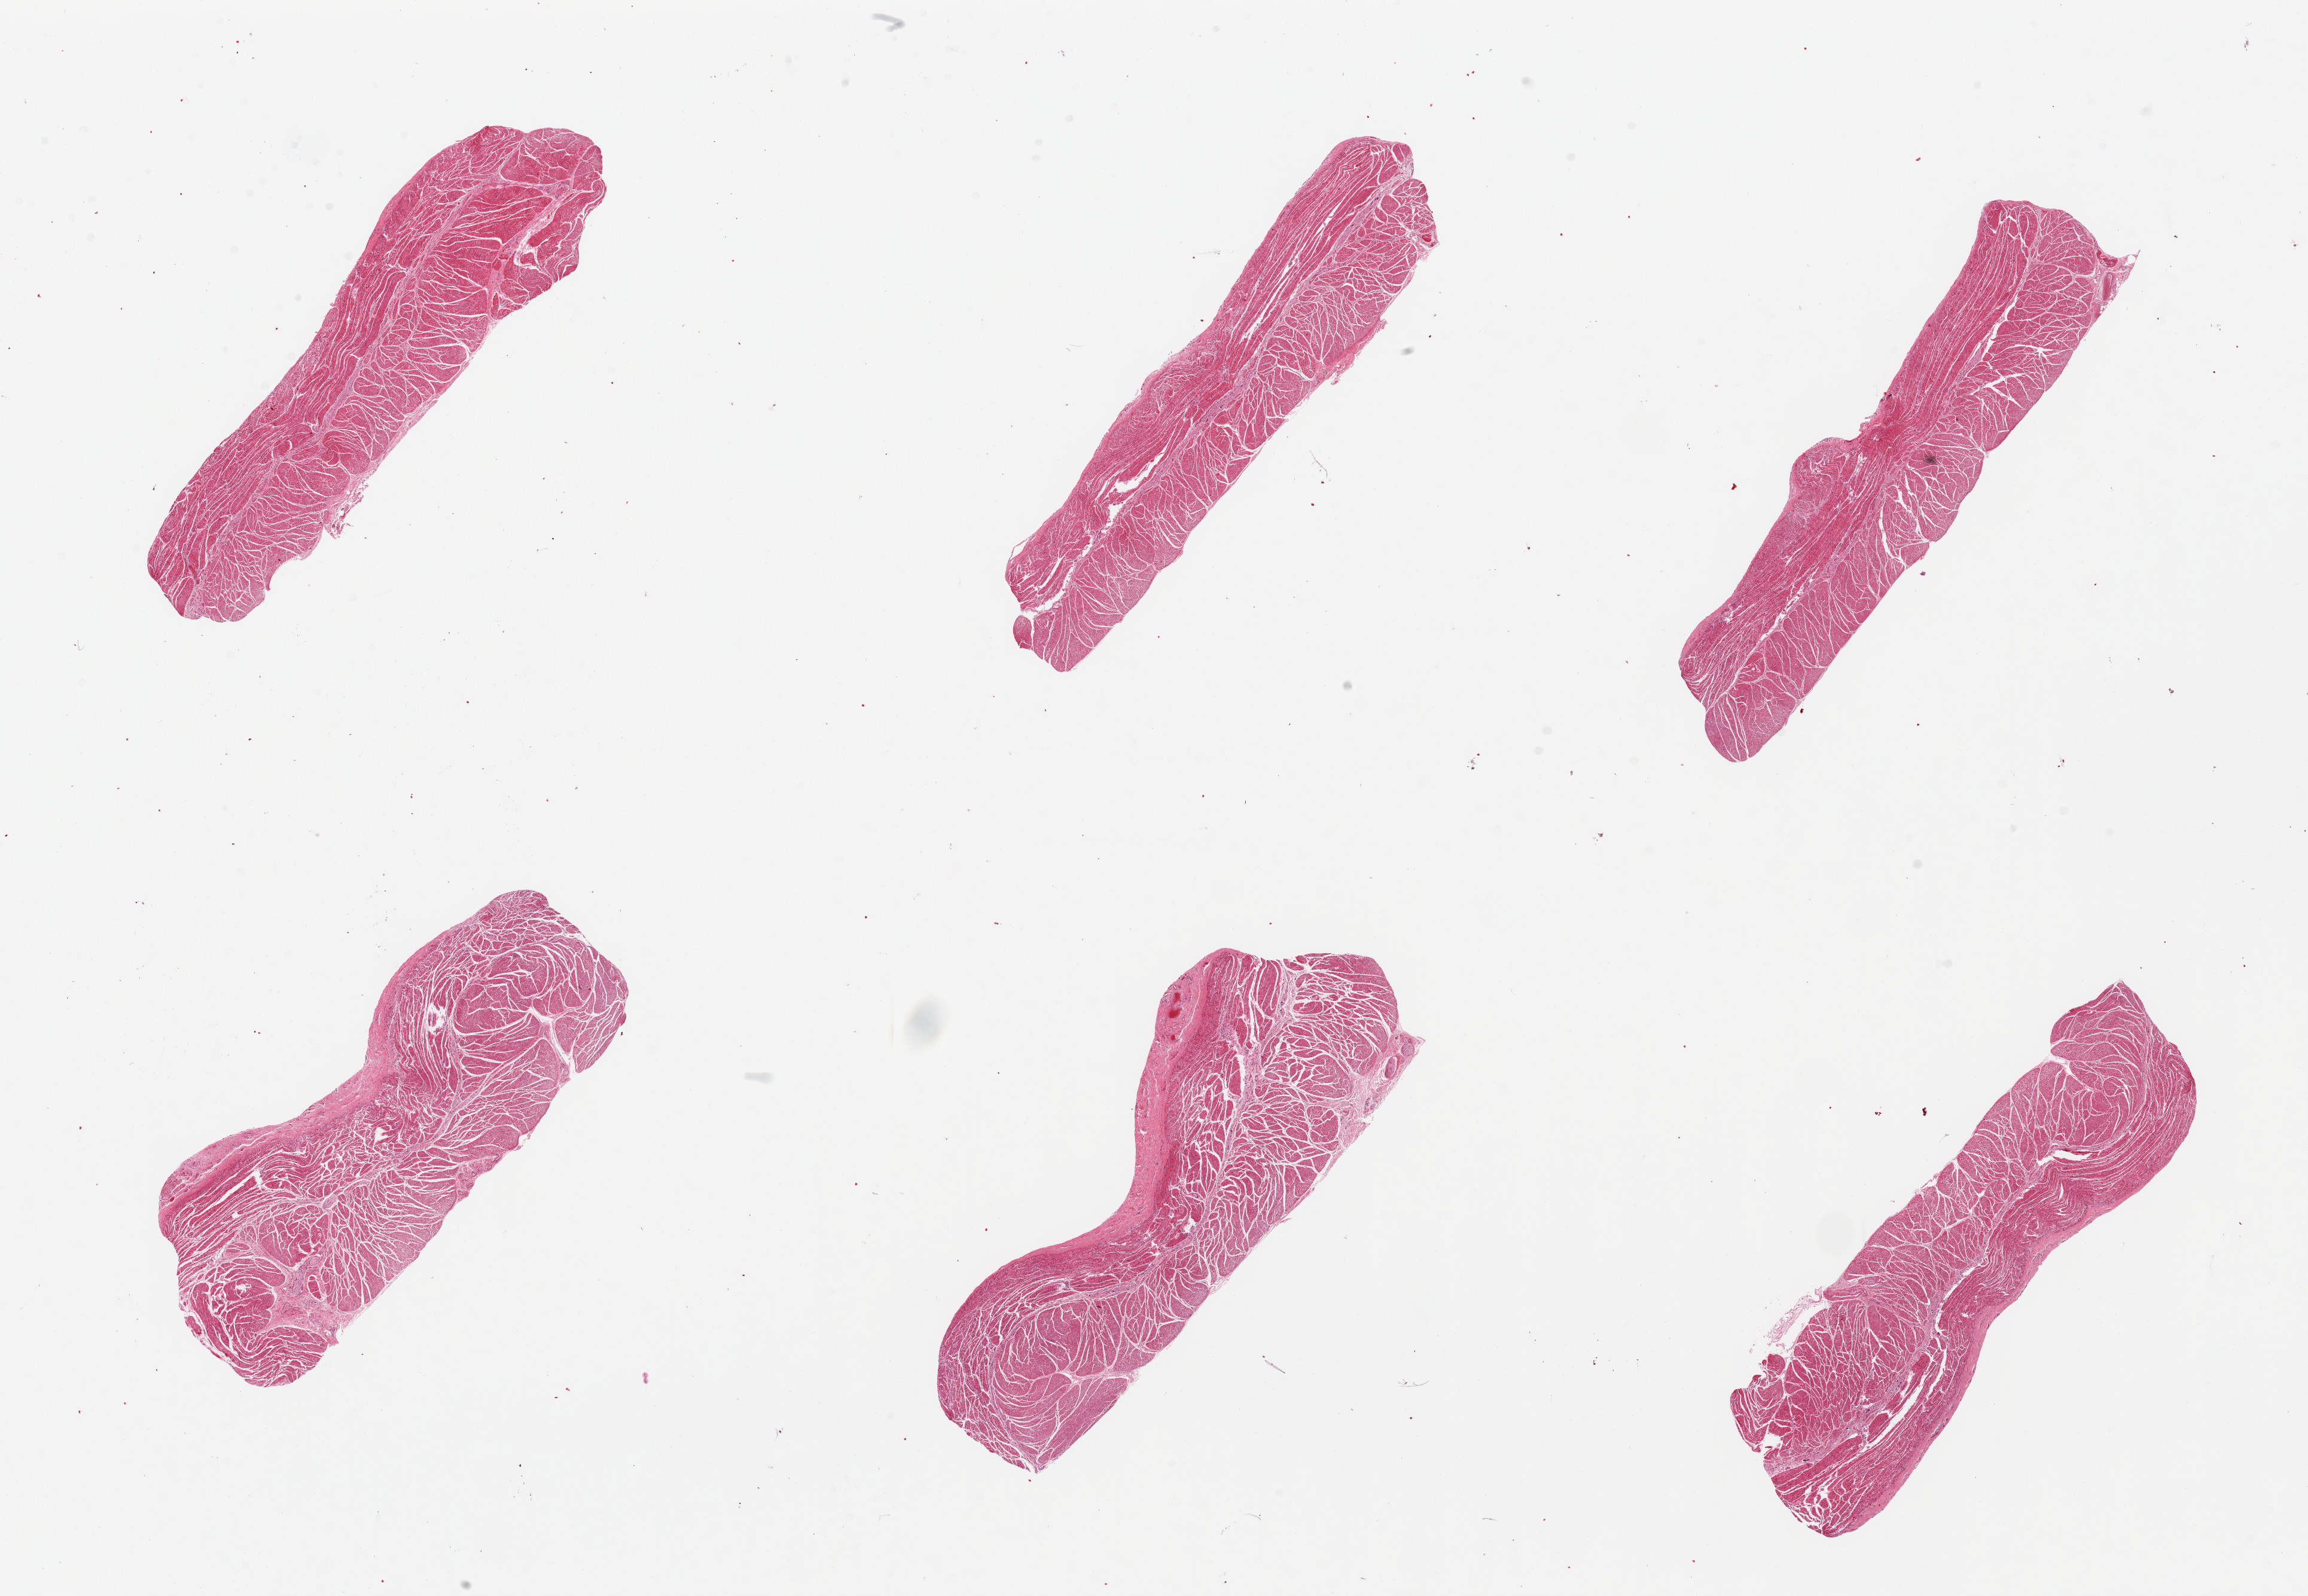
Hematoxylin and eosin (H&E) whole-slide image, brightfield — whole scanned area (about 30.5 x 21.1 mm, acquisition: 20x scan) shown as a low-resolution overview. PAXgene-fixed, paraffin-embedded tissue. Section of esophageal muscle (target tissue). Donor tissue sample. Donor sex: female.
Review note (as recorded): 6 pieces, all muscularis, good specimens.